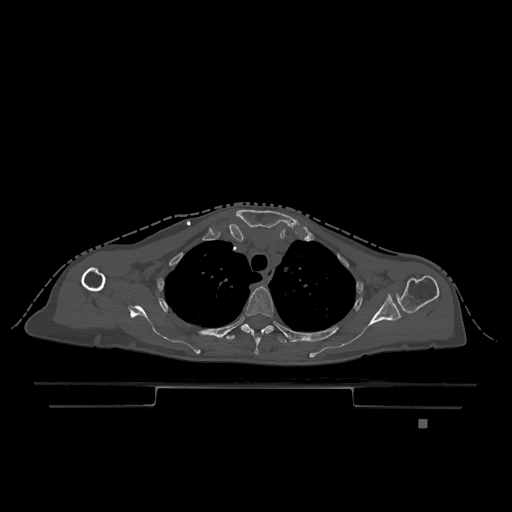
CT including the spine, one axial slice. Position 910 of 1317 along the scan axis. Bone window (W 1800 / L 400 HU). 512 × 512 image matrix. Patient: female, 74 years. Case-level facts recorded for this patient, not image findings: primary cancer: lung.
Structures marked on this image (semi-automatically segmented with operator editing):
- T3 vertebra: bounding box [x1, y1, x2, y2] px = [240, 286, 274, 355]
- T4 vertebra: [226, 324, 307, 343]